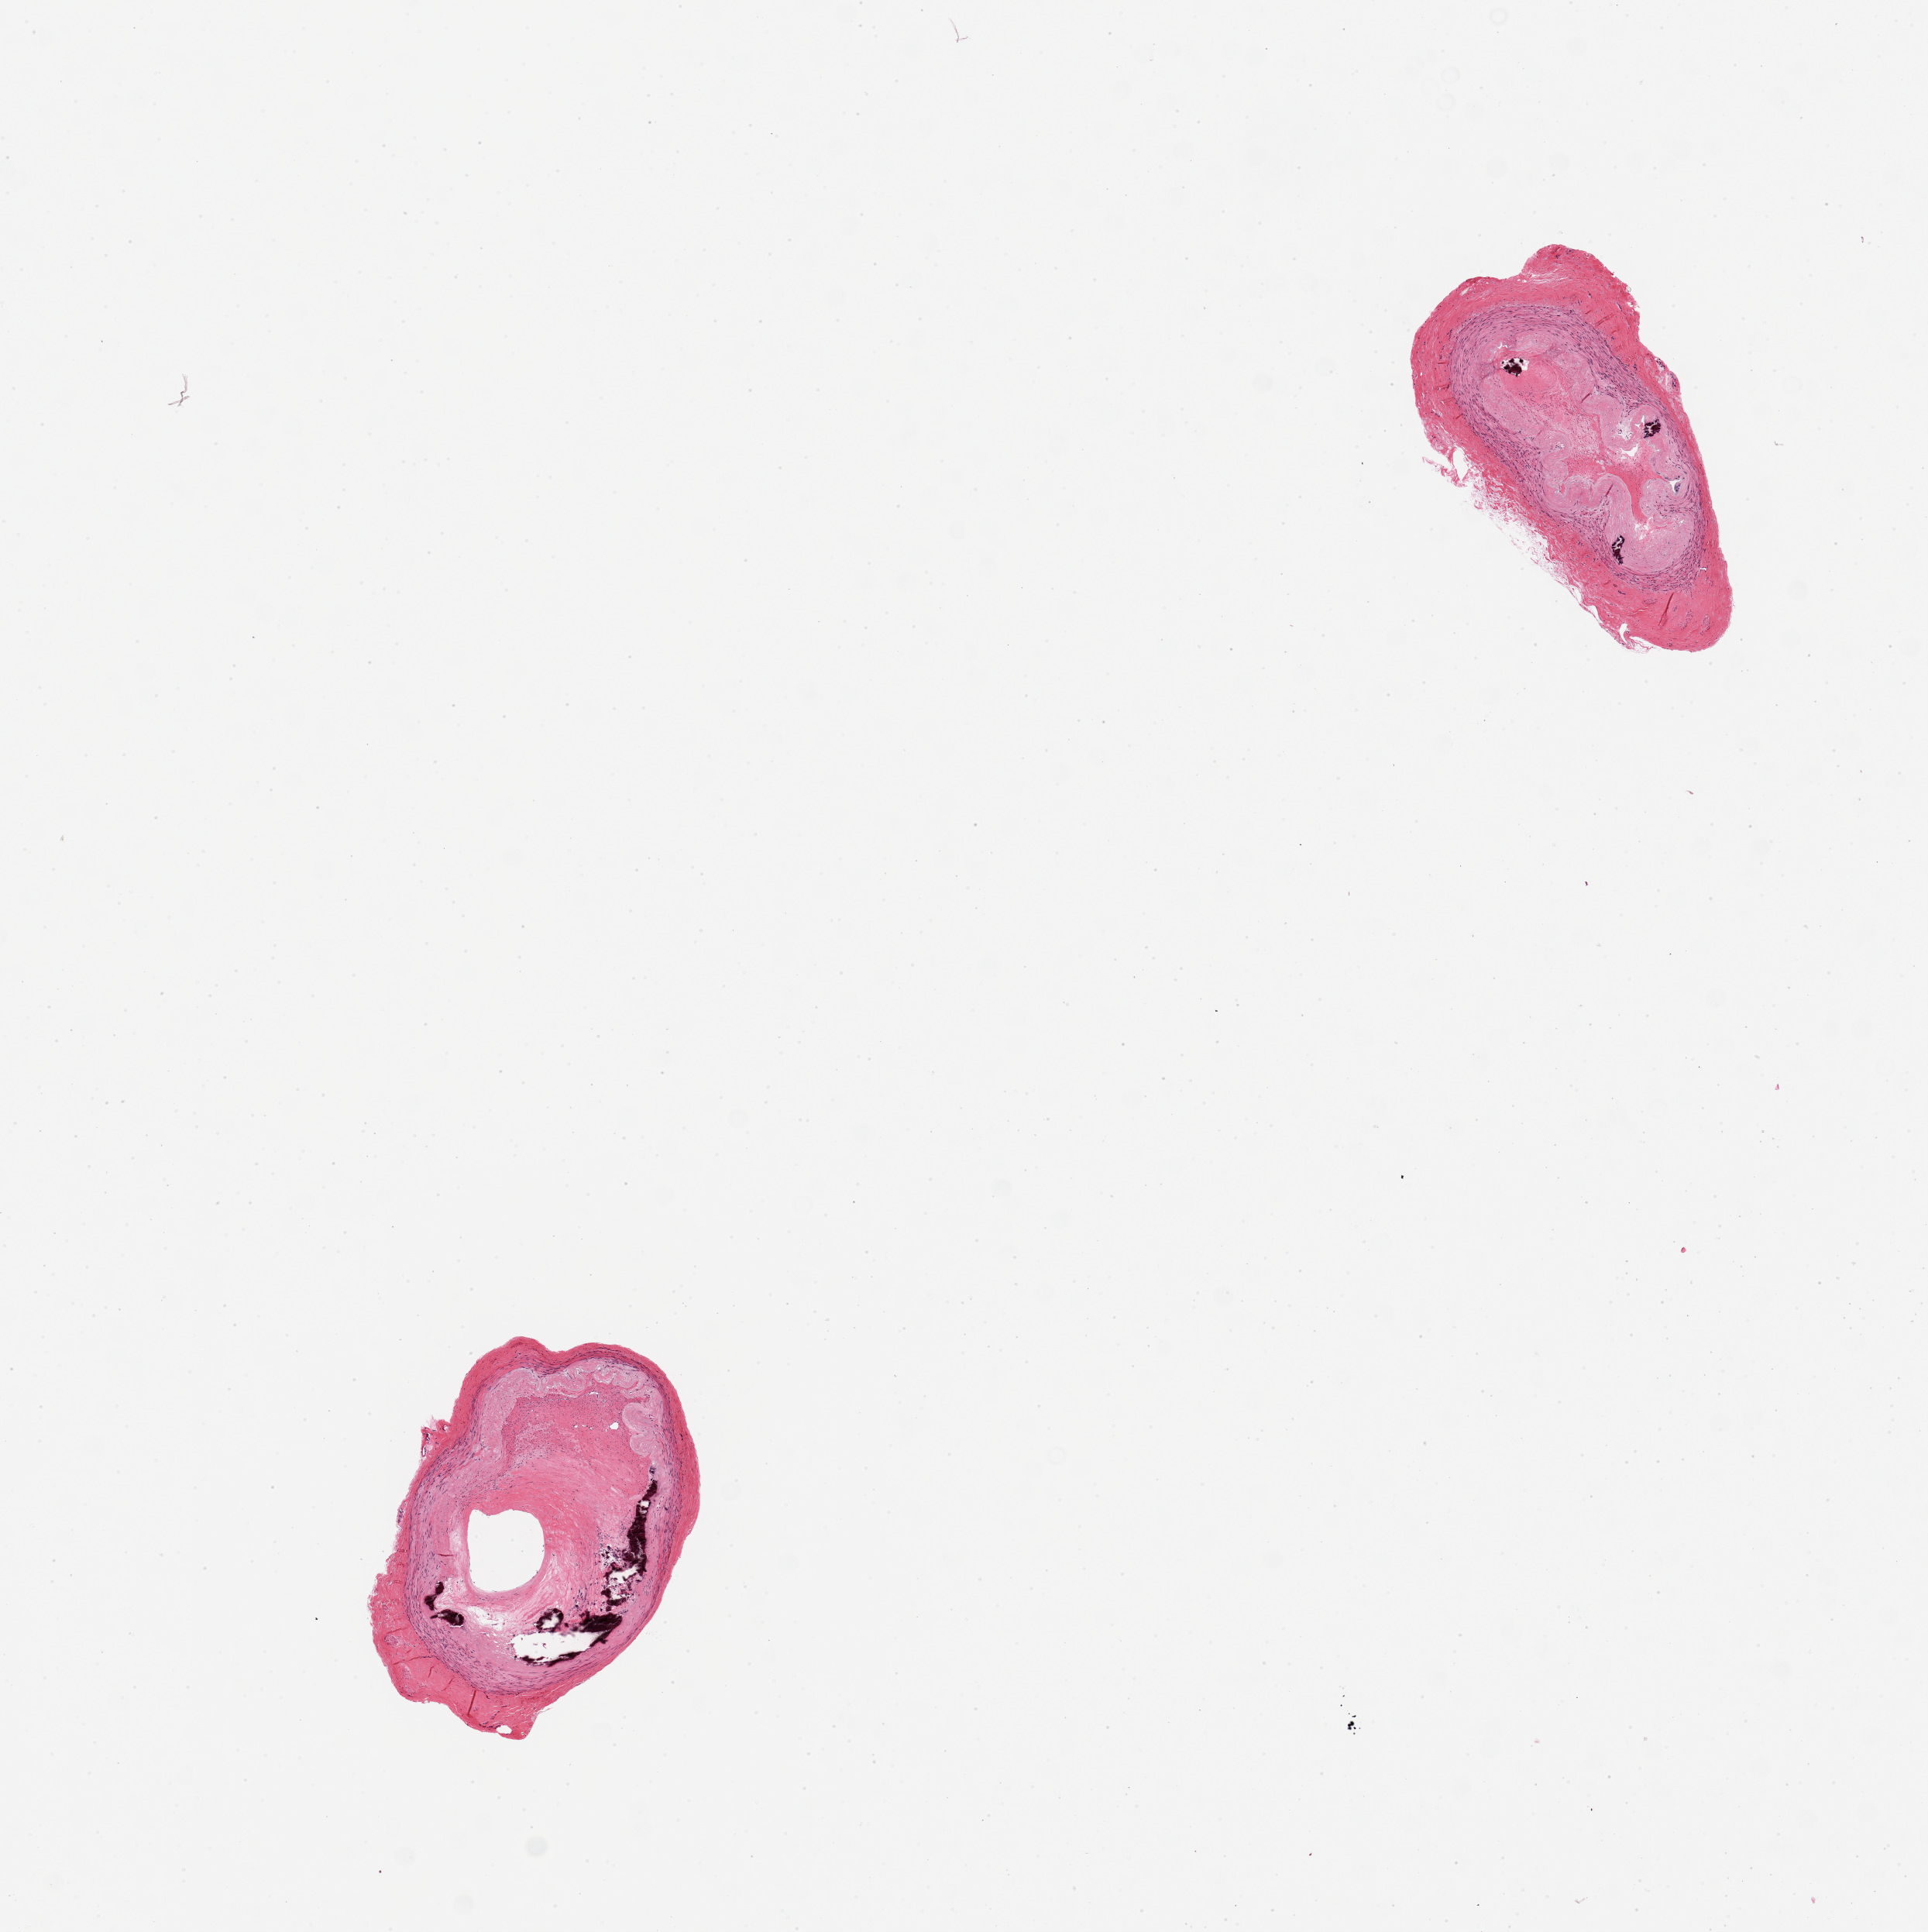
Hematoxylin and eosin (H&E) whole-slide image, brightfield — shown as a low-resolution overview of the whole scanned area (about 9.8 x 9.9 mm, from a 20x scan). PAXgene-fixed, paraffin-embedded tissue. Target tissue: tibial artery. Donor tissue sample. Donor sex: female.
* pathologist's review note for this sample: 2 pieces, clean, Monckebeg medial sclerosis